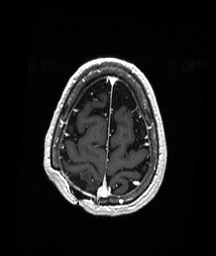
Brain MRI from a brain-tumour surgery series, one axial slice; slice 49 of 192 in the series (ordered by position); T1-weighted post-contrast; 1 mm slice thickness; 216 × 256 image matrix, field of view 211 × 250 mm. From the clinical record (not read from this slice): histopathology: Astrocytoma; WHO grade: 3.
Outlined on this slice (expert manual segmentation):
- previous resection cavity: bounding box <67,174,87,190> (left, top, right, bottom; pixels)